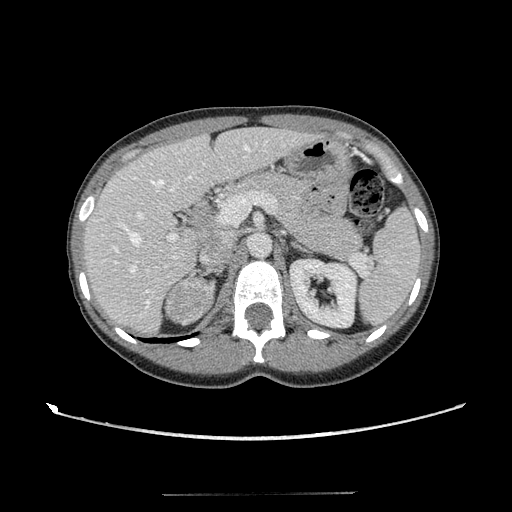
Contrast-enhanced abdominal CT, one axial slice. Position 72 of 117 along the scan axis. Reconstruction kernel STANDARD. Intravenous contrast given. Soft-tissue window (W 400 / L 40 HU). 512 × 512 image matrix, field of view 365 × 365 mm. Female patient, age 35 years. Case-level facts recorded for this patient, not image findings: diagnosis: adrenocortical carcinoma; tumour side: right adrenal; tumour size at pathology: 3 cm; Ki-67 index: 21 %; stage (as recorded): 3.
Annotated regions visible in this slice (semi-automatically segmented with operator editing):
- mass: bounding box <166,280,213,324> (left, top, right, bottom; pixels)